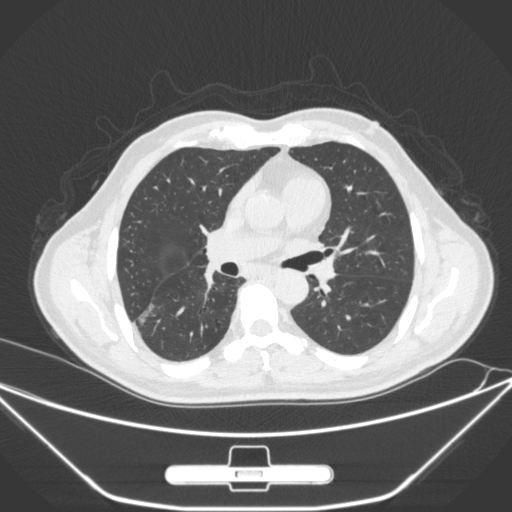
Chest CT, one axial slice. 120 kVp. Lung window (W 1500 / L -600 HU). 1 mm slice thickness. 512 × 512 image matrix. Patient: male, 71 years. Case-level facts recorded for this patient, not image findings: clinical TNM (as recorded): T1c N0 M0; histopathological grade: G2.
Annotated regions visible in this slice (rectangle marked by the reading radiologist):
- lung tumour (recorded histology: adenocarcinoma): bounding box (x1, y1, x2, y2) in pixels: (137, 303, 160, 330)